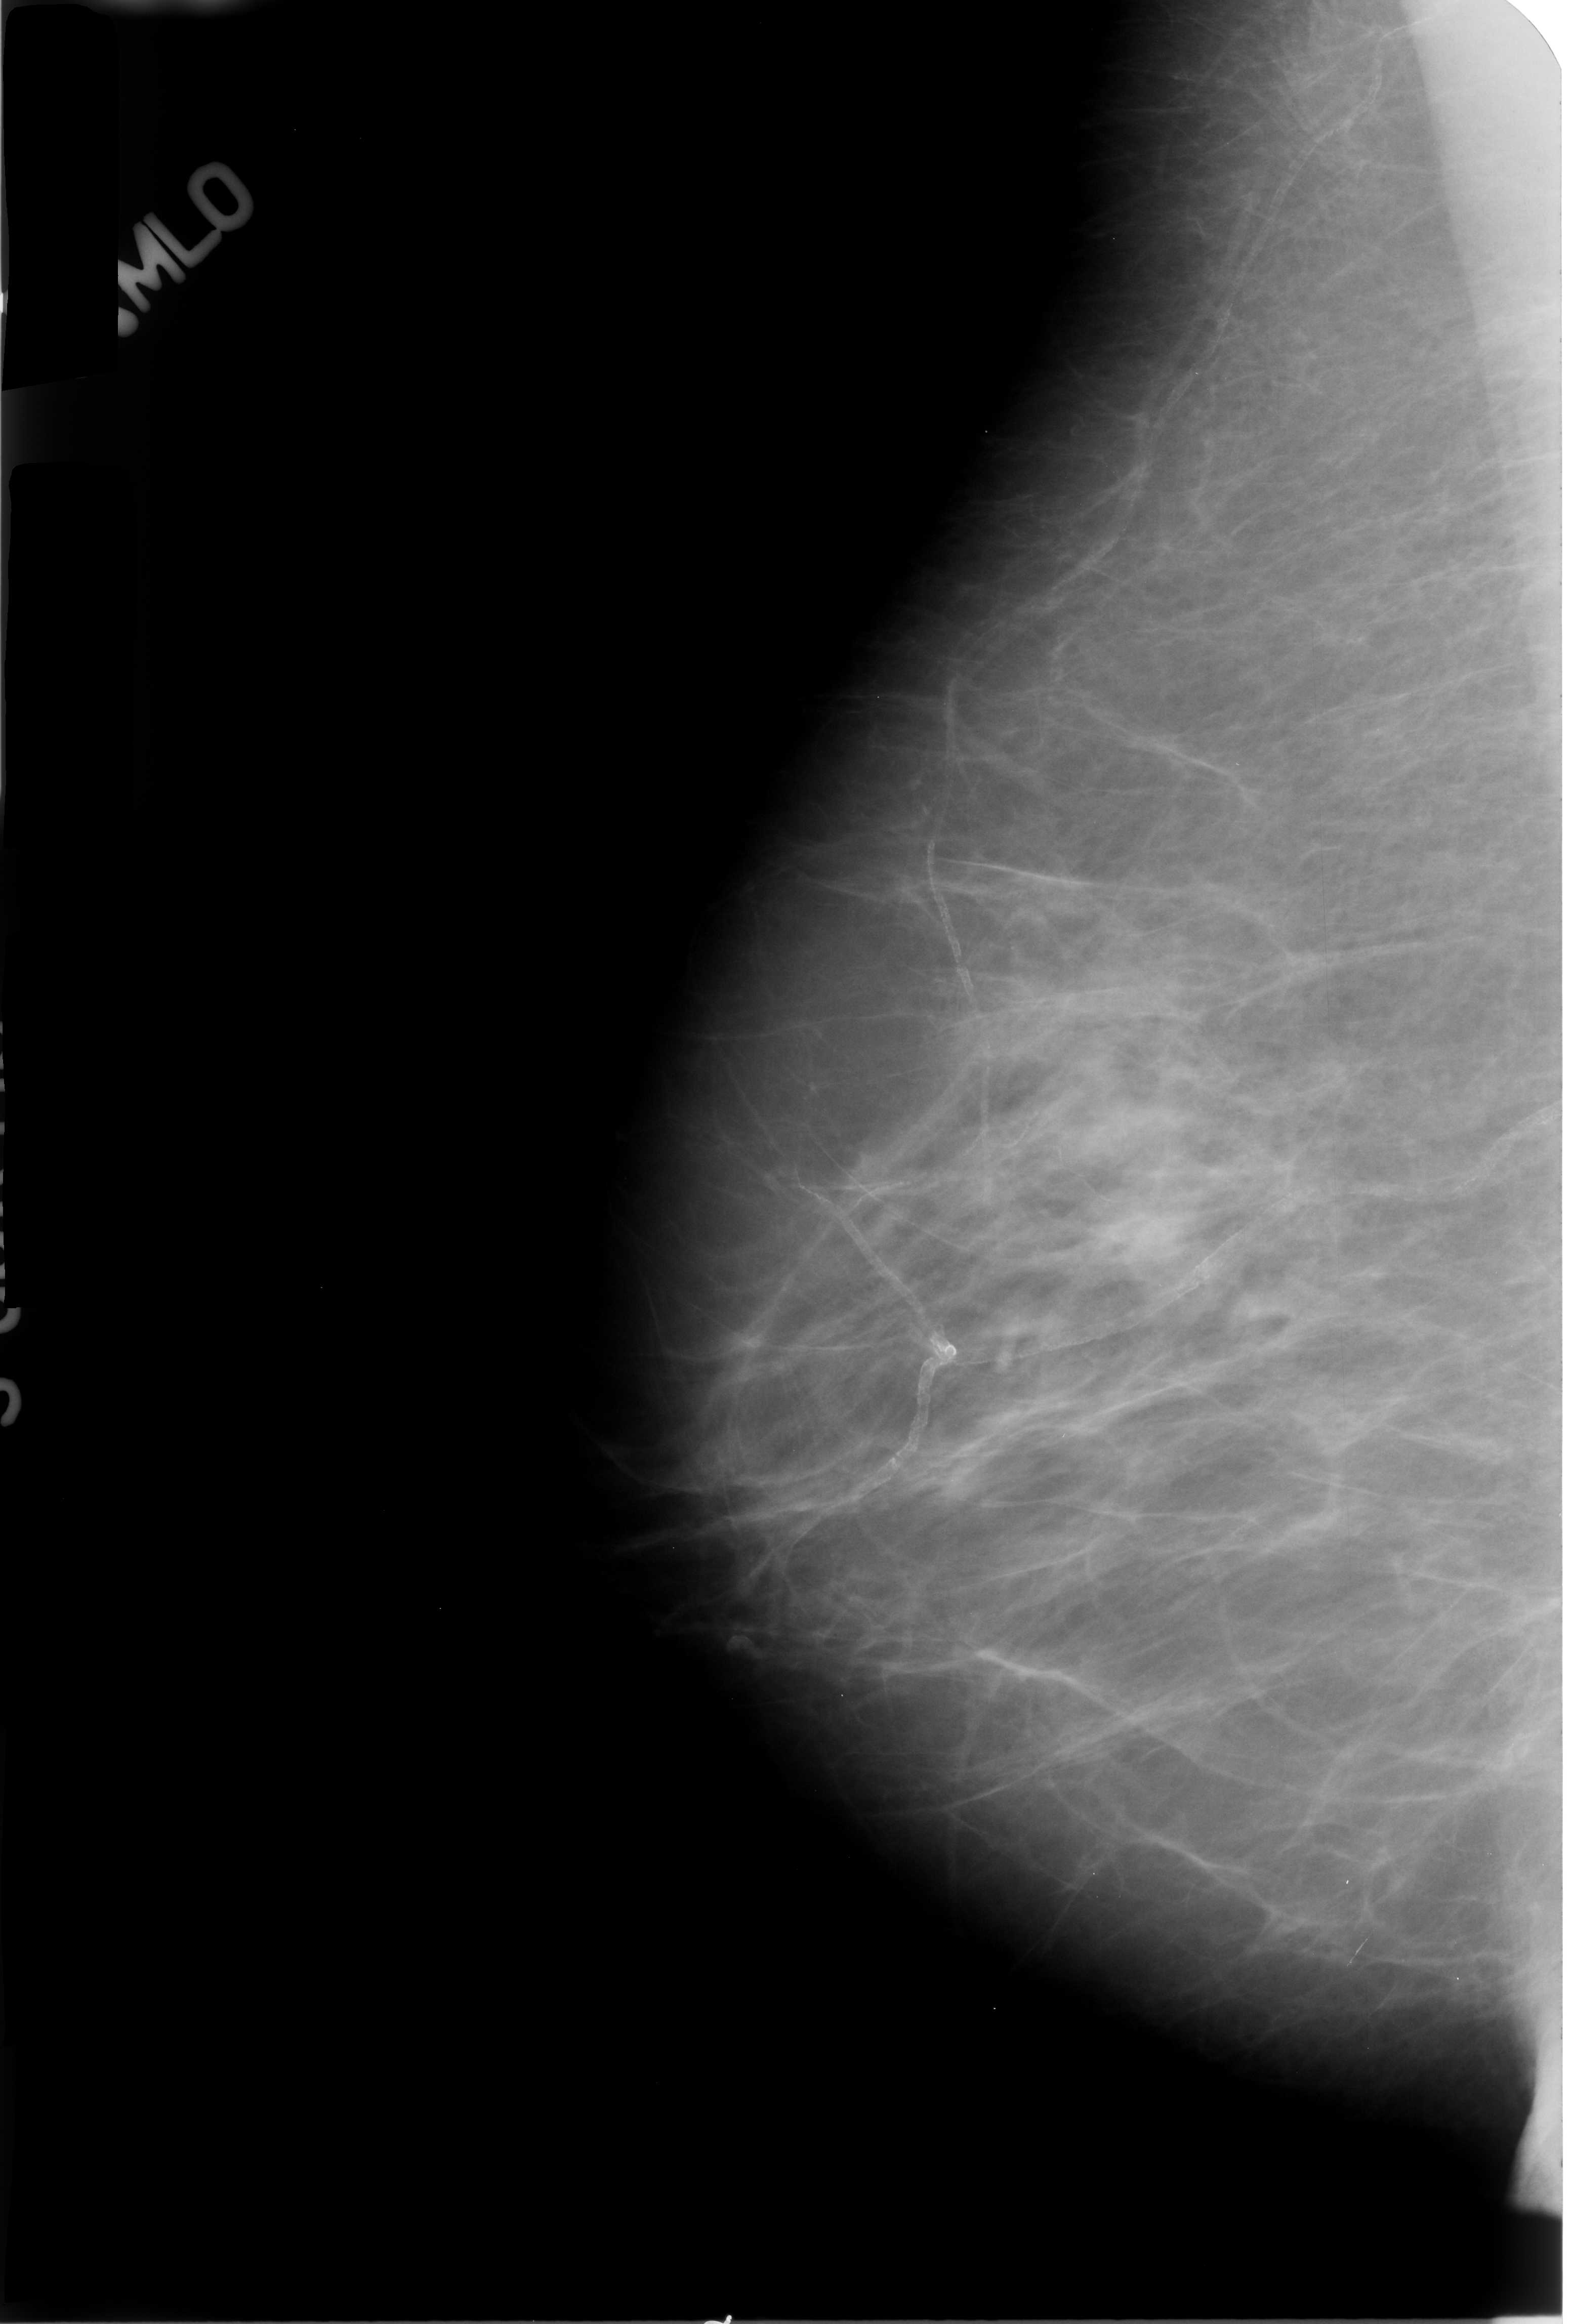
Scanned film-screen mammogram; right breast; mediolateral oblique (MLO) view; breast composition: scattered fibroglandular densities (BI-RADS density category 2 of 4); 1571 × 2324 image matrix.
Marked abnormalities (boxes around the expert regions of interest):
- Finding 1 of 3: calcifications, morphology vascular; BI-RADS assessment category 2; outcome (as recorded, no biopsy): benign without callback (not worked up further): bounding box <700,1166,936,1459> (left, top, right, bottom; pixels)
- Finding 2 of 3: calcifications, morphology vascular; BI-RADS assessment category 2; subtlety rating 3 on a 1 (subtle) to 5 (obvious) scale; outcome (as recorded, no biopsy): benign without callback (not worked up further): <716,1101,1556,1608>
- Finding 3 of 3: calcifications, morphology vascular; BI-RADS assessment category 2; benign; no additional work-up was recommended (outcome (as recorded, no biopsy): benign without callback): <923,28,1394,1236>